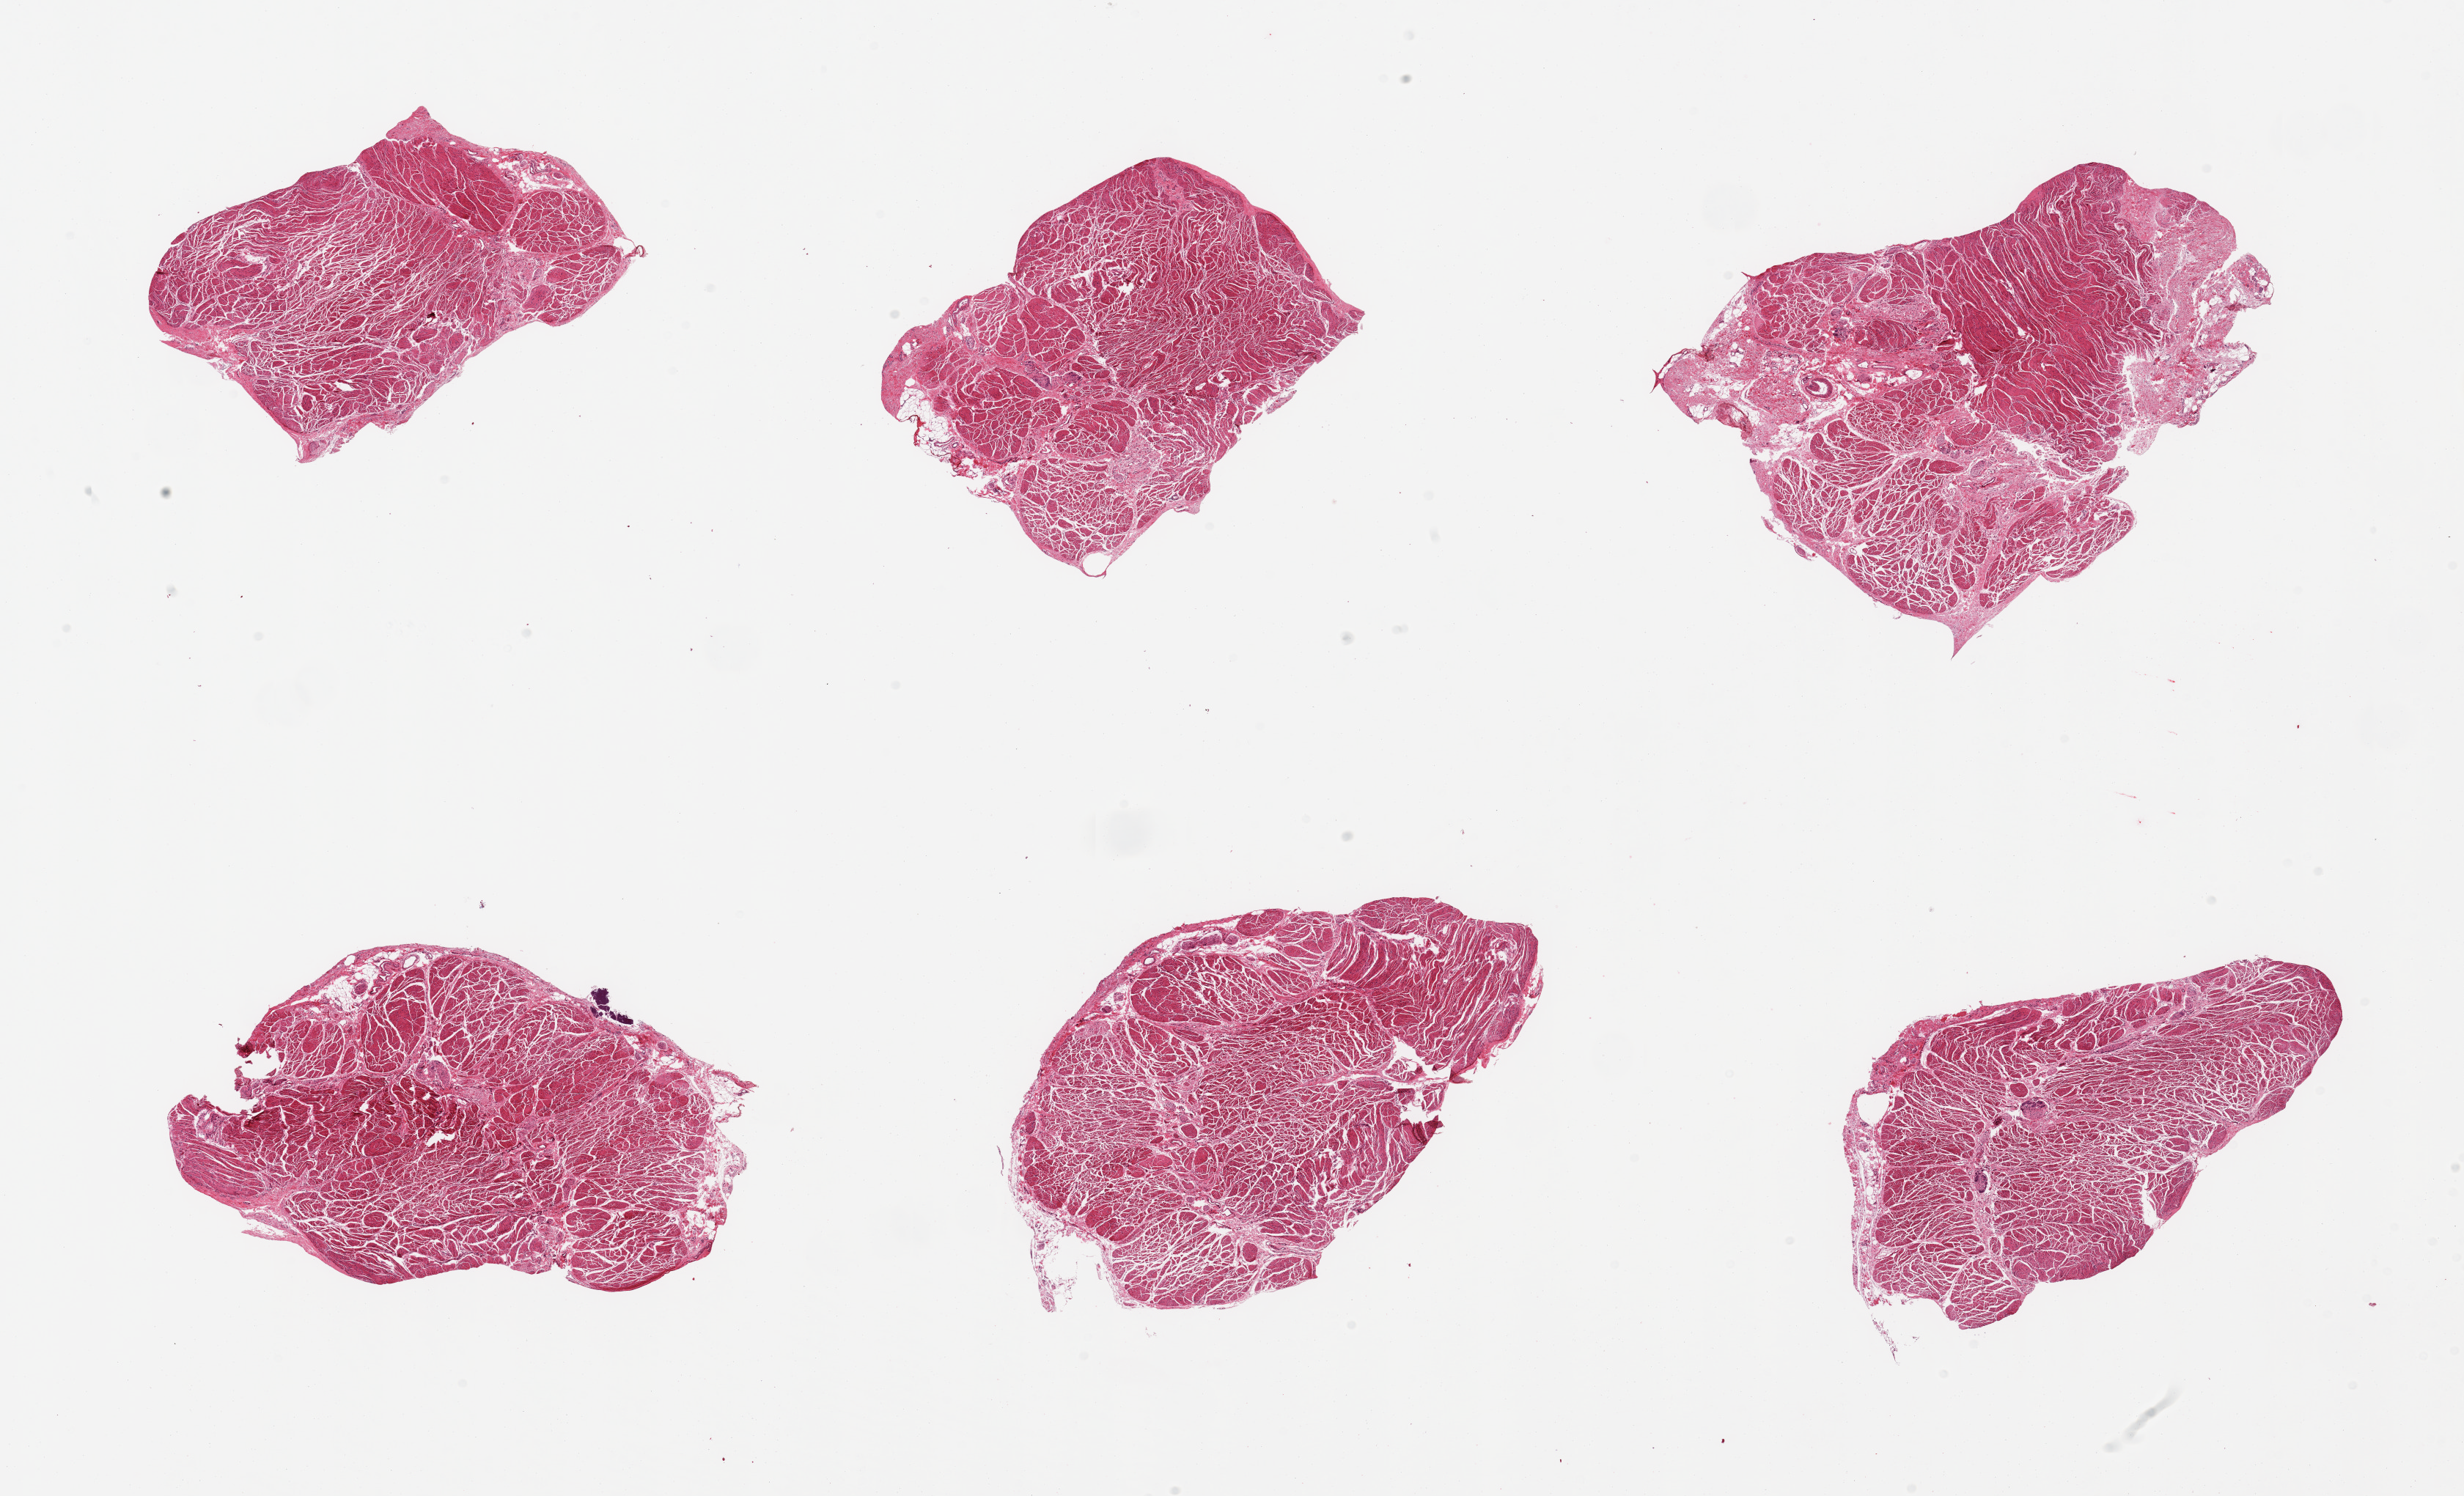
Digitized hematoxylin and eosin (H&E)-stained section — a low-resolution overview of the entire scanned area, about 26.6 x 16.1 mm (from a 20x scan); PAXgene-fixed, paraffin-embedded tissue; target tissue: esophageal muscle; tissue donor sample. Donor sex: female.
* reviewer comment on this tissue sample: 6 pieces; well dissected